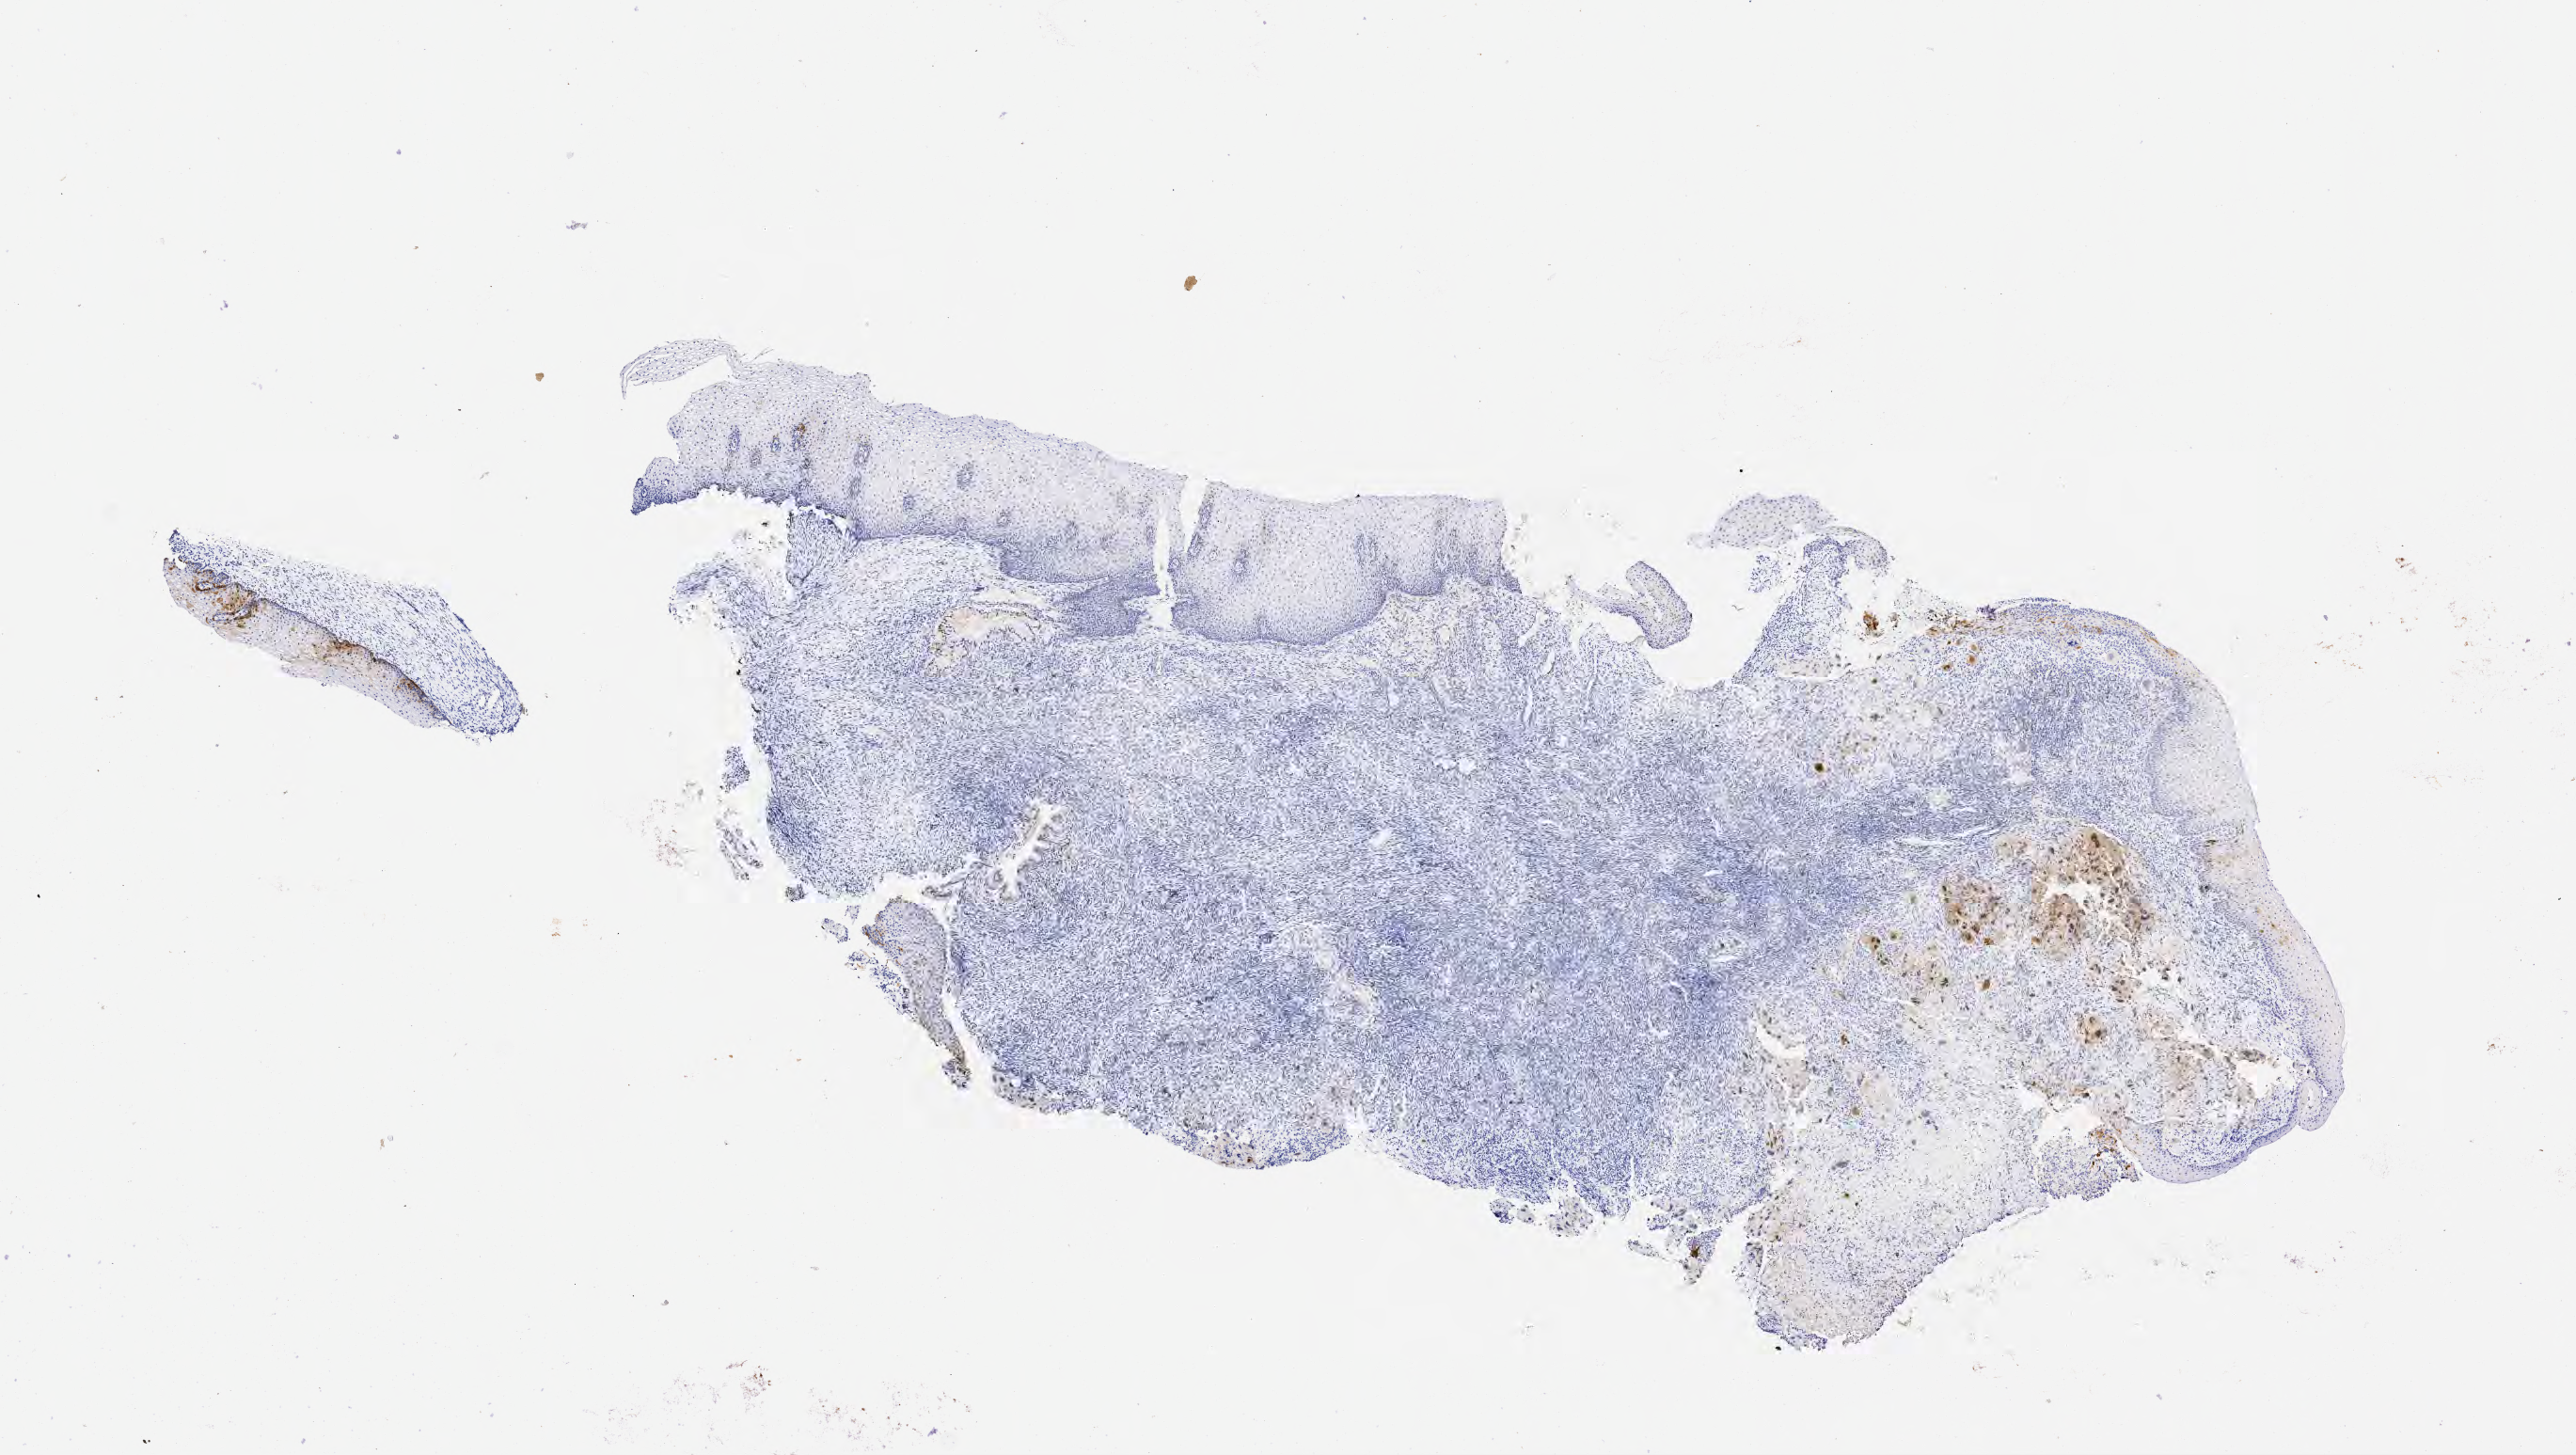
Whole-slide image, immunohistochemical stain for p16 (p16INK4a) — shown as a low-resolution overview of the whole scanned area (about 11.1 x 6.2 mm); tumor tissue; anatomic site: cervix. Female patient, 46 years old.
Diagnosis: Squamous cell carcinoma, large cell, nonkeratinizing, NOS.